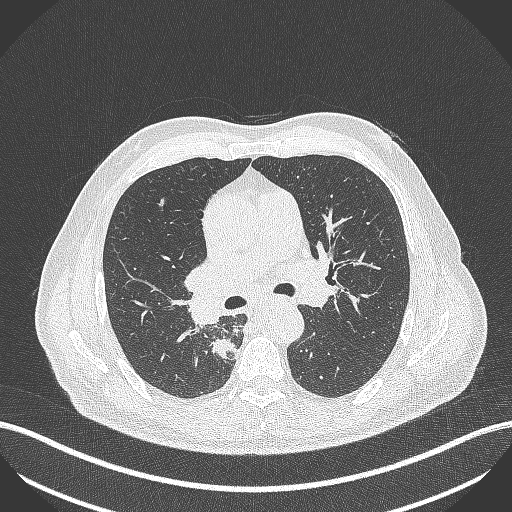
Chest CT, one axial slice; position 280 of 451 along the scan axis; reconstruction kernel B70f; 100 kVp; lung window (W 1500 / L -600 HU); 512 × 512 image matrix. Patient: male, 61 years. From the clinical record (not read from this slice): clinical TNM (as recorded): T1 N0 M0; histopathological grade: G3.
Outlined on this slice (rectangle marked by the reading radiologist):
- lung tumour (recorded histology: small cell carcinoma): bounding box [x1, y1, x2, y2] px = [210, 336, 239, 361]